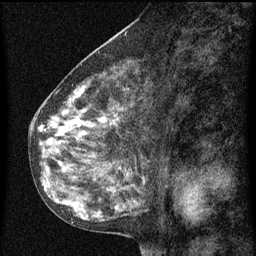
Breast MRI (dynamic contrast-enhanced), one sagittal slice; position 37 of 60 along the scan axis; dynamic contrast-enhanced series, image 2 of 3 at this slice position (ordered by acquisition); 1.5 T; TE 4.2 ms, TR 8 ms; 256 × 256 image matrix, field of view 180 × 180 mm. Female patient, age 55 years.
Structures marked on this image (semi-automatically segmented with operator editing):
- analysis volume of interest (the breast-tissue region the enhancement analysis was run in; not a lesion): bounding box <34,68,149,151> (left, top, right, bottom; pixels)
- tumour enhancement mask (voxels above the 70 % enhancement threshold inside the analysis volume of interest): <38,84,119,151>